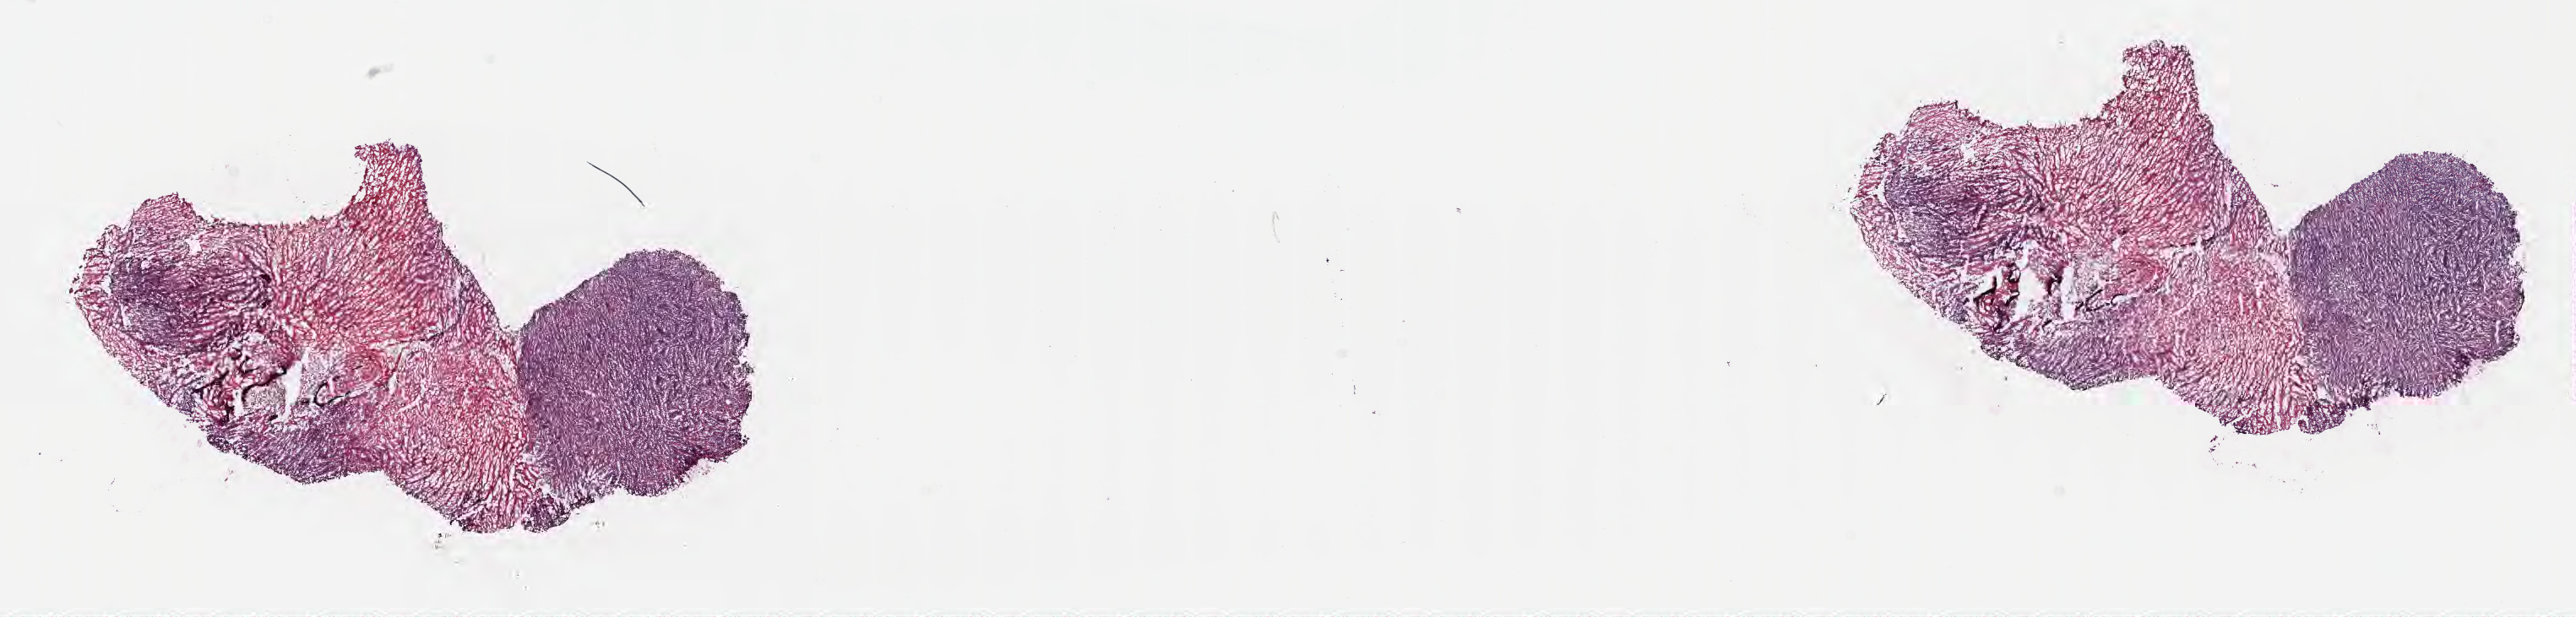
Hematoxylin and eosin (H&E) whole-slide image, shown as a low-resolution overview of the whole scanned area (about 24.7 x 5.9 mm), frozen section, primary tumor, anatomic site: cranium. Patient: male, 11 years old. Pathologist review of this section (percent, as recorded): tumor cells 40%, tumor nuclei 90%, stromal cells 10%, necrosis 50%, normal cells 0%. Infiltration values recorded for this section: lymphocyte infiltration 50%, monocyte infiltration 30%, neutrophil infiltration 5%.
Ann Arbor stage (patient): Stage III. Histologic diagnosis: Diffuse large B-cell lymphoma, NOS.